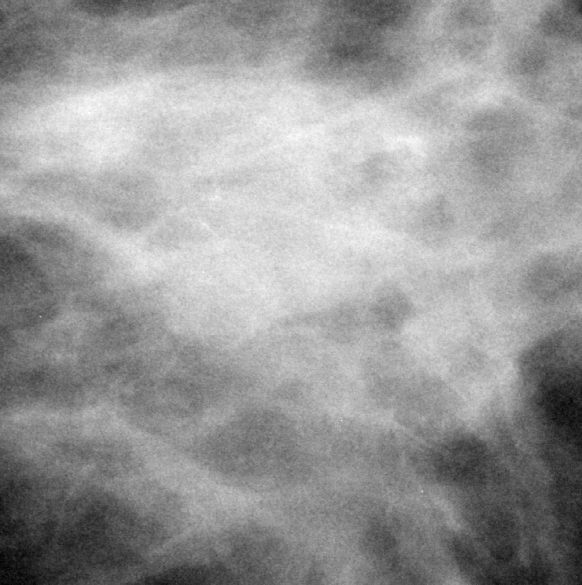
Cropped region of a digitized screen-film mammogram centred on a radiologist-marked abnormality, left breast, CC view.
- Finding: mass, shape irregular, margins ill defined; BI-RADS assessment category 4; subtlety rating 4 on a 1 (subtle) to 5 (obvious) scale; pathology (as recorded): malignant.